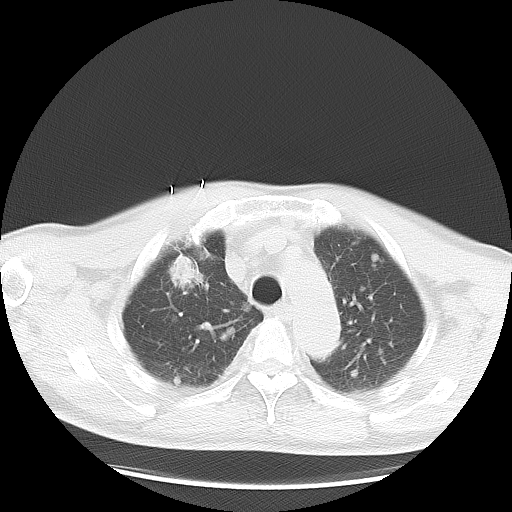
Chest CT, one axial slice; slice 24 of 36 in the series (ordered by position); 120 kVp; lung window (W 1500 / L -600 HU); 5 mm slice thickness; 512 × 512 image matrix. Patient: male, 57 years. From the clinical record (not read from this slice): clinical TNM (as recorded): T2 N3 M1a.
Outlined on this slice (rectangle marked by the reading radiologist):
- lung tumour (recorded histology: adenocarcinoma): bounding box [x1, y1, x2, y2] px = [163, 250, 204, 295]